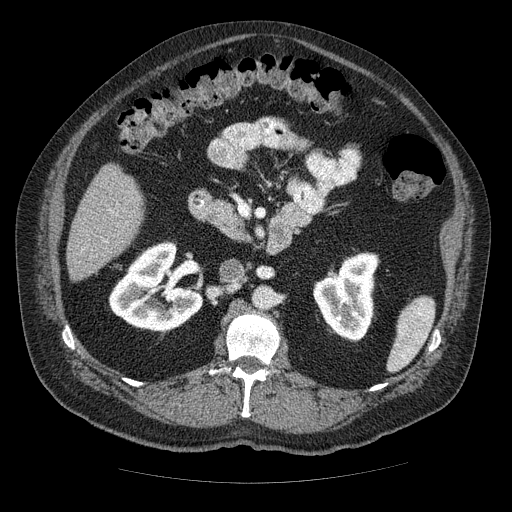
Contrast-enhanced abdominal CT (liver protocol), one axial slice; slice 16 of 85 in the series (ordered by position); reconstruction kernel STANDARD; 120 kVp; soft-tissue window (W 400 / L 40 HU); 2.5 mm slice thickness; 512 × 512 image matrix, field of view 420 × 420 mm. Case-level facts recorded for this patient, not image findings: diagnosis: hepatocellular carcinoma (patient treated with transarterial chemoembolisation; whether this scan precedes or follows treatment is not stated here); TNM stage (as recorded): Stage-IIIA; Child-Pugh class: A; tumour nodularity: multinodular; tumour size: 7 cm.
Annotated regions visible in this slice (semi-automatic segmentation, software-assisted and operator-edited):
- liver parenchyma outside the tumour (the mass and vessels are separate outlines, so this box may not span the whole liver): bounding box [x1, y1, x2, y2] px = [66, 164, 143, 280]